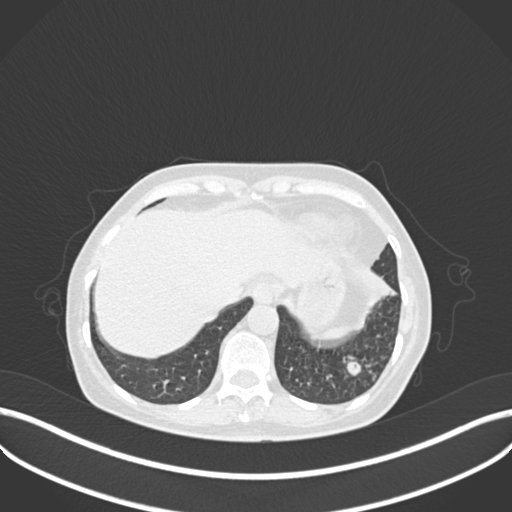
Chest CT, one axial slice. Slice 45 of 270 in the series (ordered by position). Reconstruction kernel B30f. 120 kVp. Lung window (W 1500 / L -600 HU). 512 × 512 image matrix, field of view 400 × 400 mm. Patient: female, 63 years. Case-level facts recorded for this patient, not image findings: clinical TNM (as recorded): T1b N0 M0; histopathological grade: G2-3.
Outlined on this slice (bounding box drawn by a radiologist):
- lung tumour (recorded histology: adenocarcinoma): bounding box <362,265,393,308> (left, top, right, bottom; pixels)